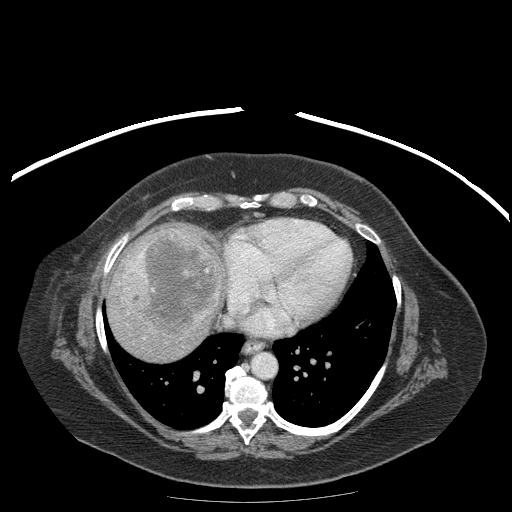
Contrast-enhanced abdominal CT (liver protocol), one axial slice. Slice 167 of 204 in the series (ordered by position). Reconstruction kernel STANDARD. 120 kVp. Soft-tissue window (W 400 / L 40 HU). 512 × 512 image matrix, field of view 440 × 440 mm. From the clinical record (not read from this slice): diagnosis: hepatocellular carcinoma (patient treated with transarterial chemoembolisation; whether this scan precedes or follows treatment is not stated here); TNM stage (as recorded): Stage-IIIB; Child-Pugh class: A; tumour differentiation: well differentiated.
Annotated regions visible in this slice (semi-automatically segmented with operator editing):
- liver parenchyma outside the tumour (the mass and vessels are separate outlines, so this box may not span the whole liver): box from (x=102, y=224) to (x=222, y=360) px
- mass: (x=119, y=231)–(x=224, y=339)